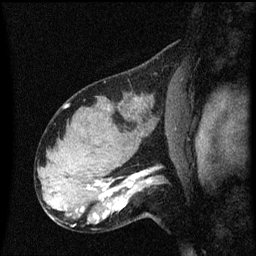
Breast MRI (dynamic contrast-enhanced), one sagittal slice; slice 39 of 60 in the series (ordered by position); dynamic contrast-enhanced series, image 2 of 3 at this slice position (ordered by acquisition); 1.5 T; TE 4.2 ms, TR 8.4 ms; 2 mm slice thickness; 256 × 256 image matrix, field of view 200 × 200 mm. Female patient, age 31 years. Case-level facts recorded for this patient, not image findings: setting: breast cancer imaged before/during neoadjuvant chemotherapy; receptor status: HR-positive, HER2-negative.
Annotated regions visible in this slice (semi-automatically segmented with operator editing):
- analysis volume of interest (the breast-tissue region the enhancement analysis was run in; not a lesion): bounding box (x1, y1, x2, y2) in pixels: (102, 166, 167, 223)
- tumour enhancement mask (voxels above the 70 % enhancement threshold inside the analysis volume of interest): (104, 170, 151, 217)